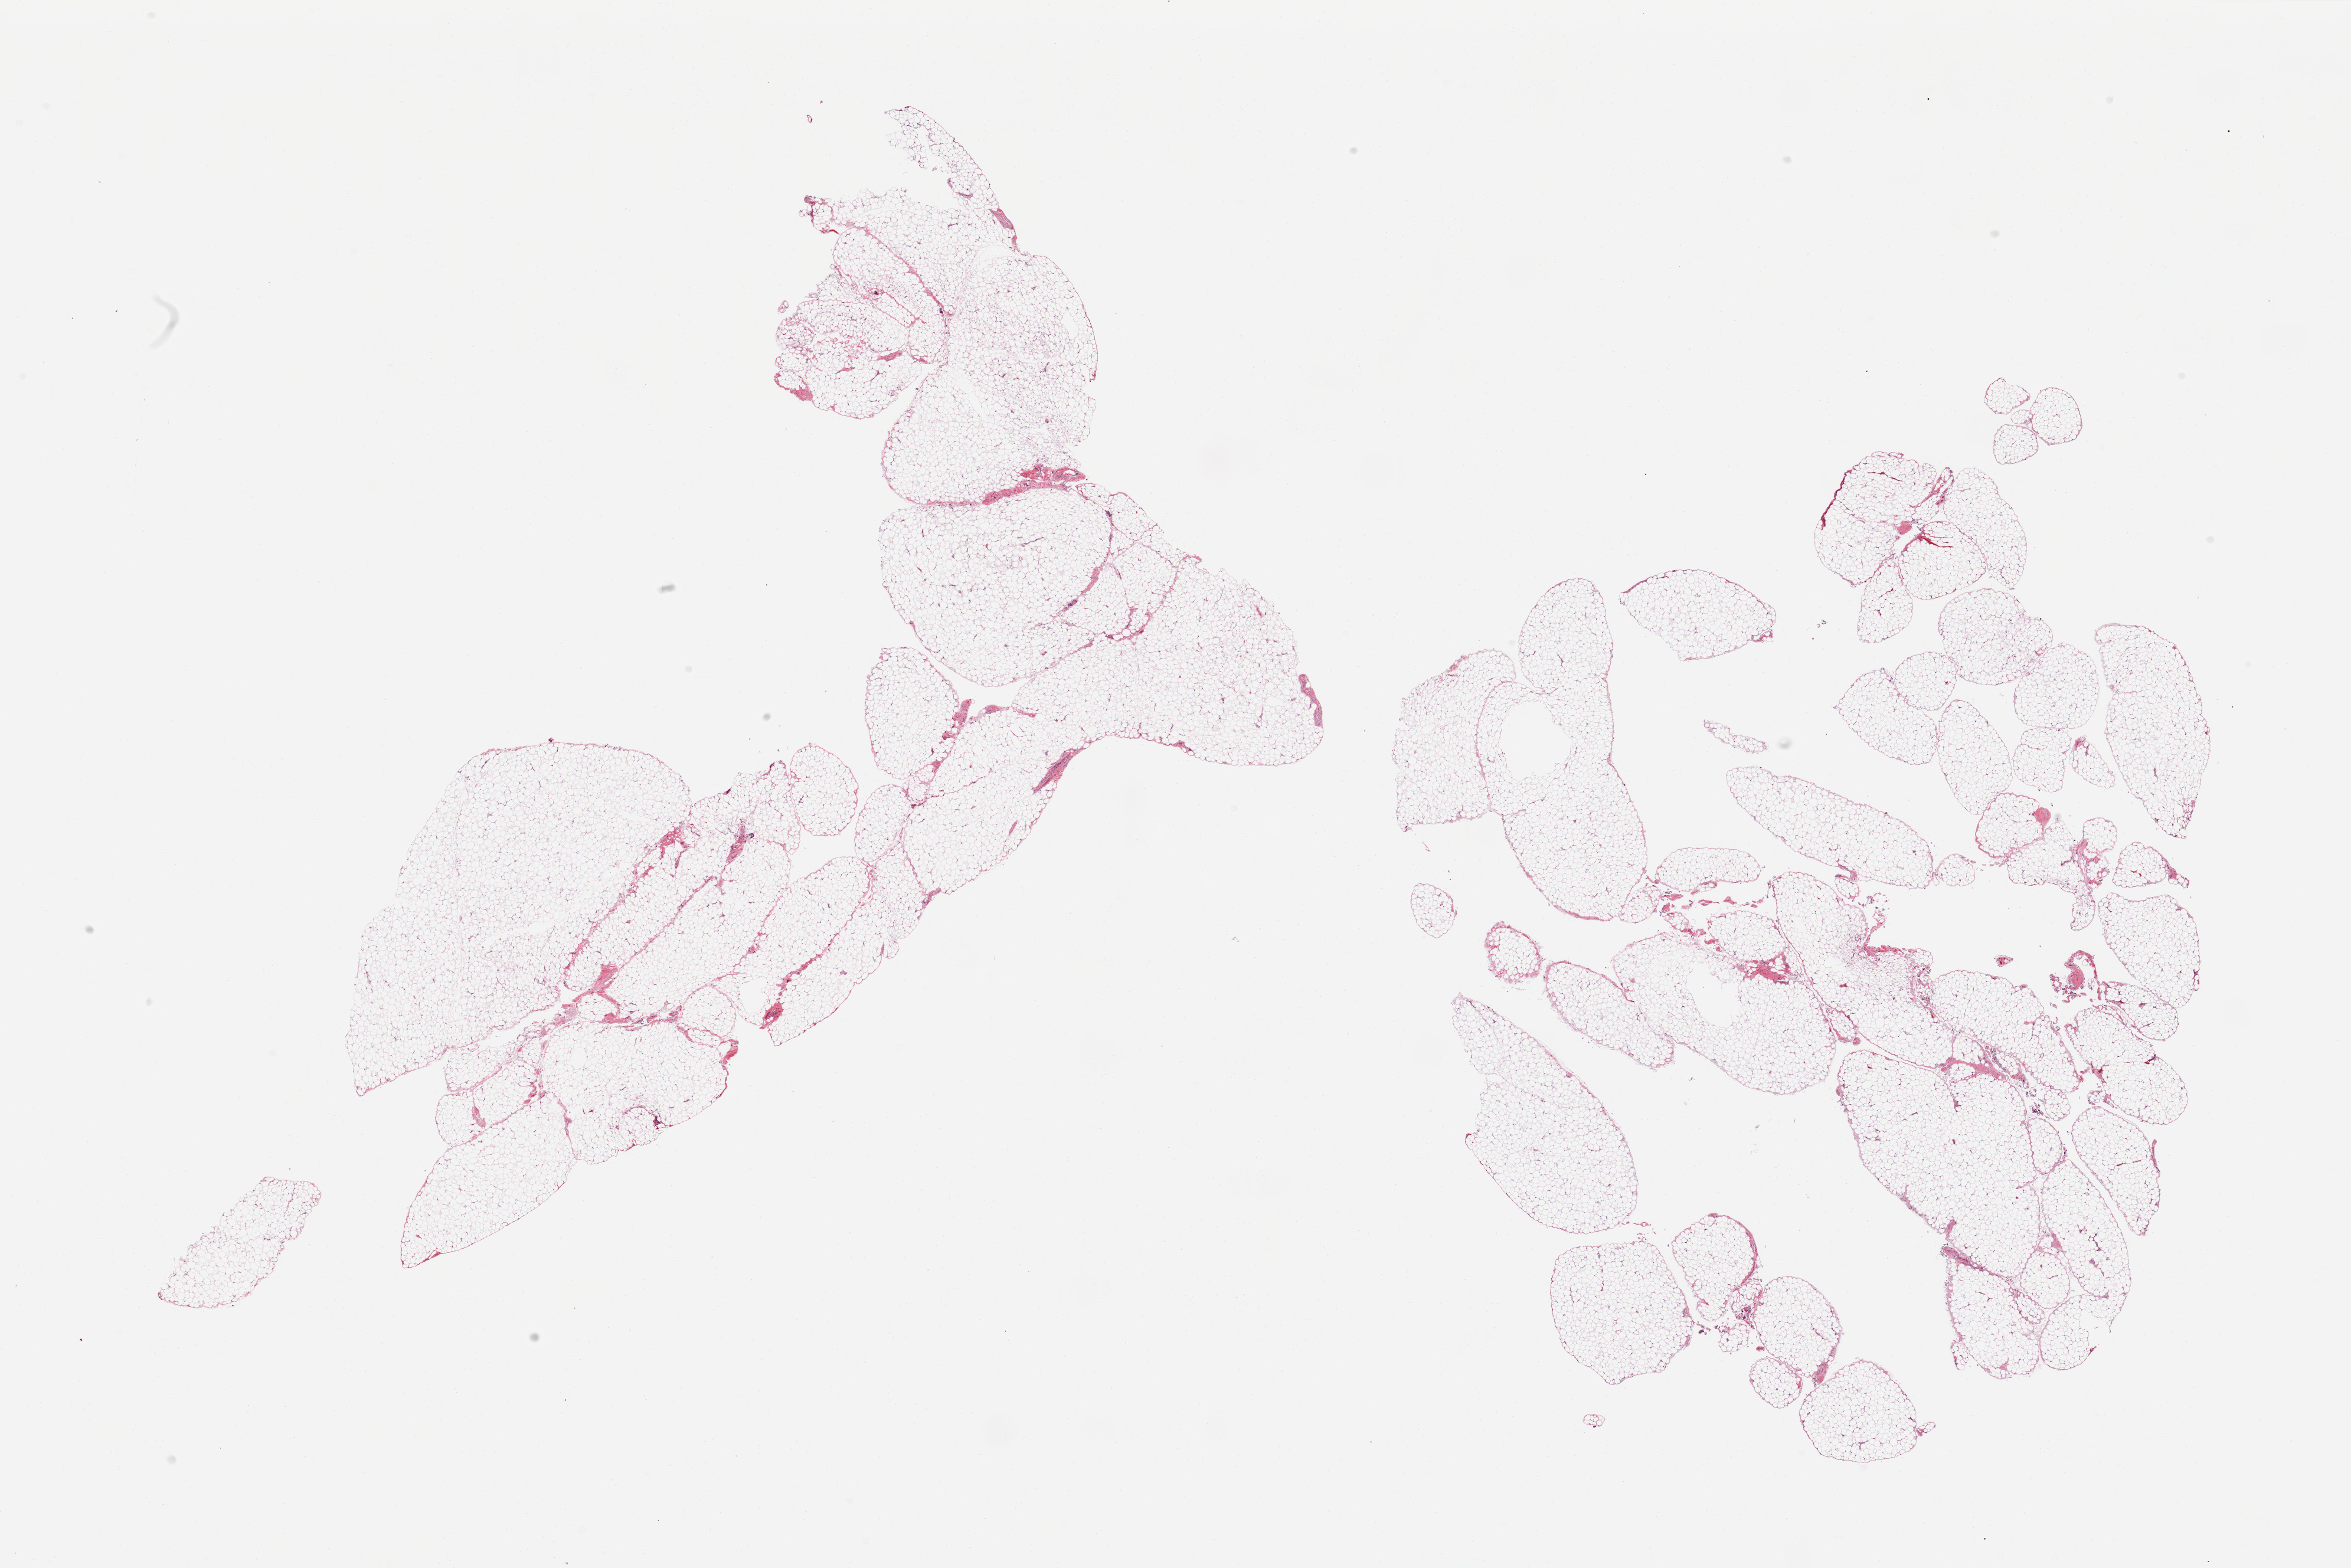
Whole-slide image, hematoxylin and eosin (H&E) stain, brightfield, low-resolution overview of the scanned area, about 31.5 x 21.0 mm (acquisition: 20x scan). PAXgene-fixed, paraffin-embedded tissue. Sampled site (target tissue): omentum. Tissue donor sample. Male donor.
Review note (as recorded): 2 pieces; lobulated mature adipose tissue.